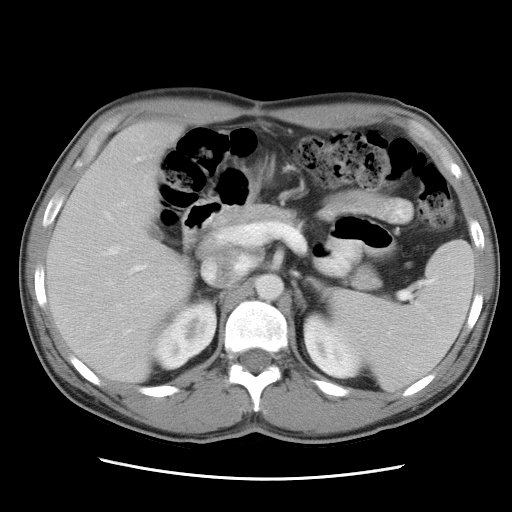
Contrast-enhanced abdominal CT, one axial slice. Position 17 of 34 along the scan axis. Intravenous contrast given. Soft-tissue window (W 400 / L 40 HU). 512 × 512 image matrix, field of view 360 × 360 mm. Male patient, age 40 years. Case-level facts recorded for this patient, not image findings: diagnosis: colorectal cancer liver metastases, imaged before liver resection; multiple liver metastases: yes; largest metastasis: 1.5 cm; disease in both lobes: yes.
Annotated regions visible in this slice (expert manual segmentation):
- liver: bounding box [x1, y1, x2, y2] px = [47, 121, 191, 381]
- planned liver remnant (the part of the liver to remain after resection): [47, 121, 191, 382]
- portal vein (with intrahepatic branches): [106, 221, 257, 274]